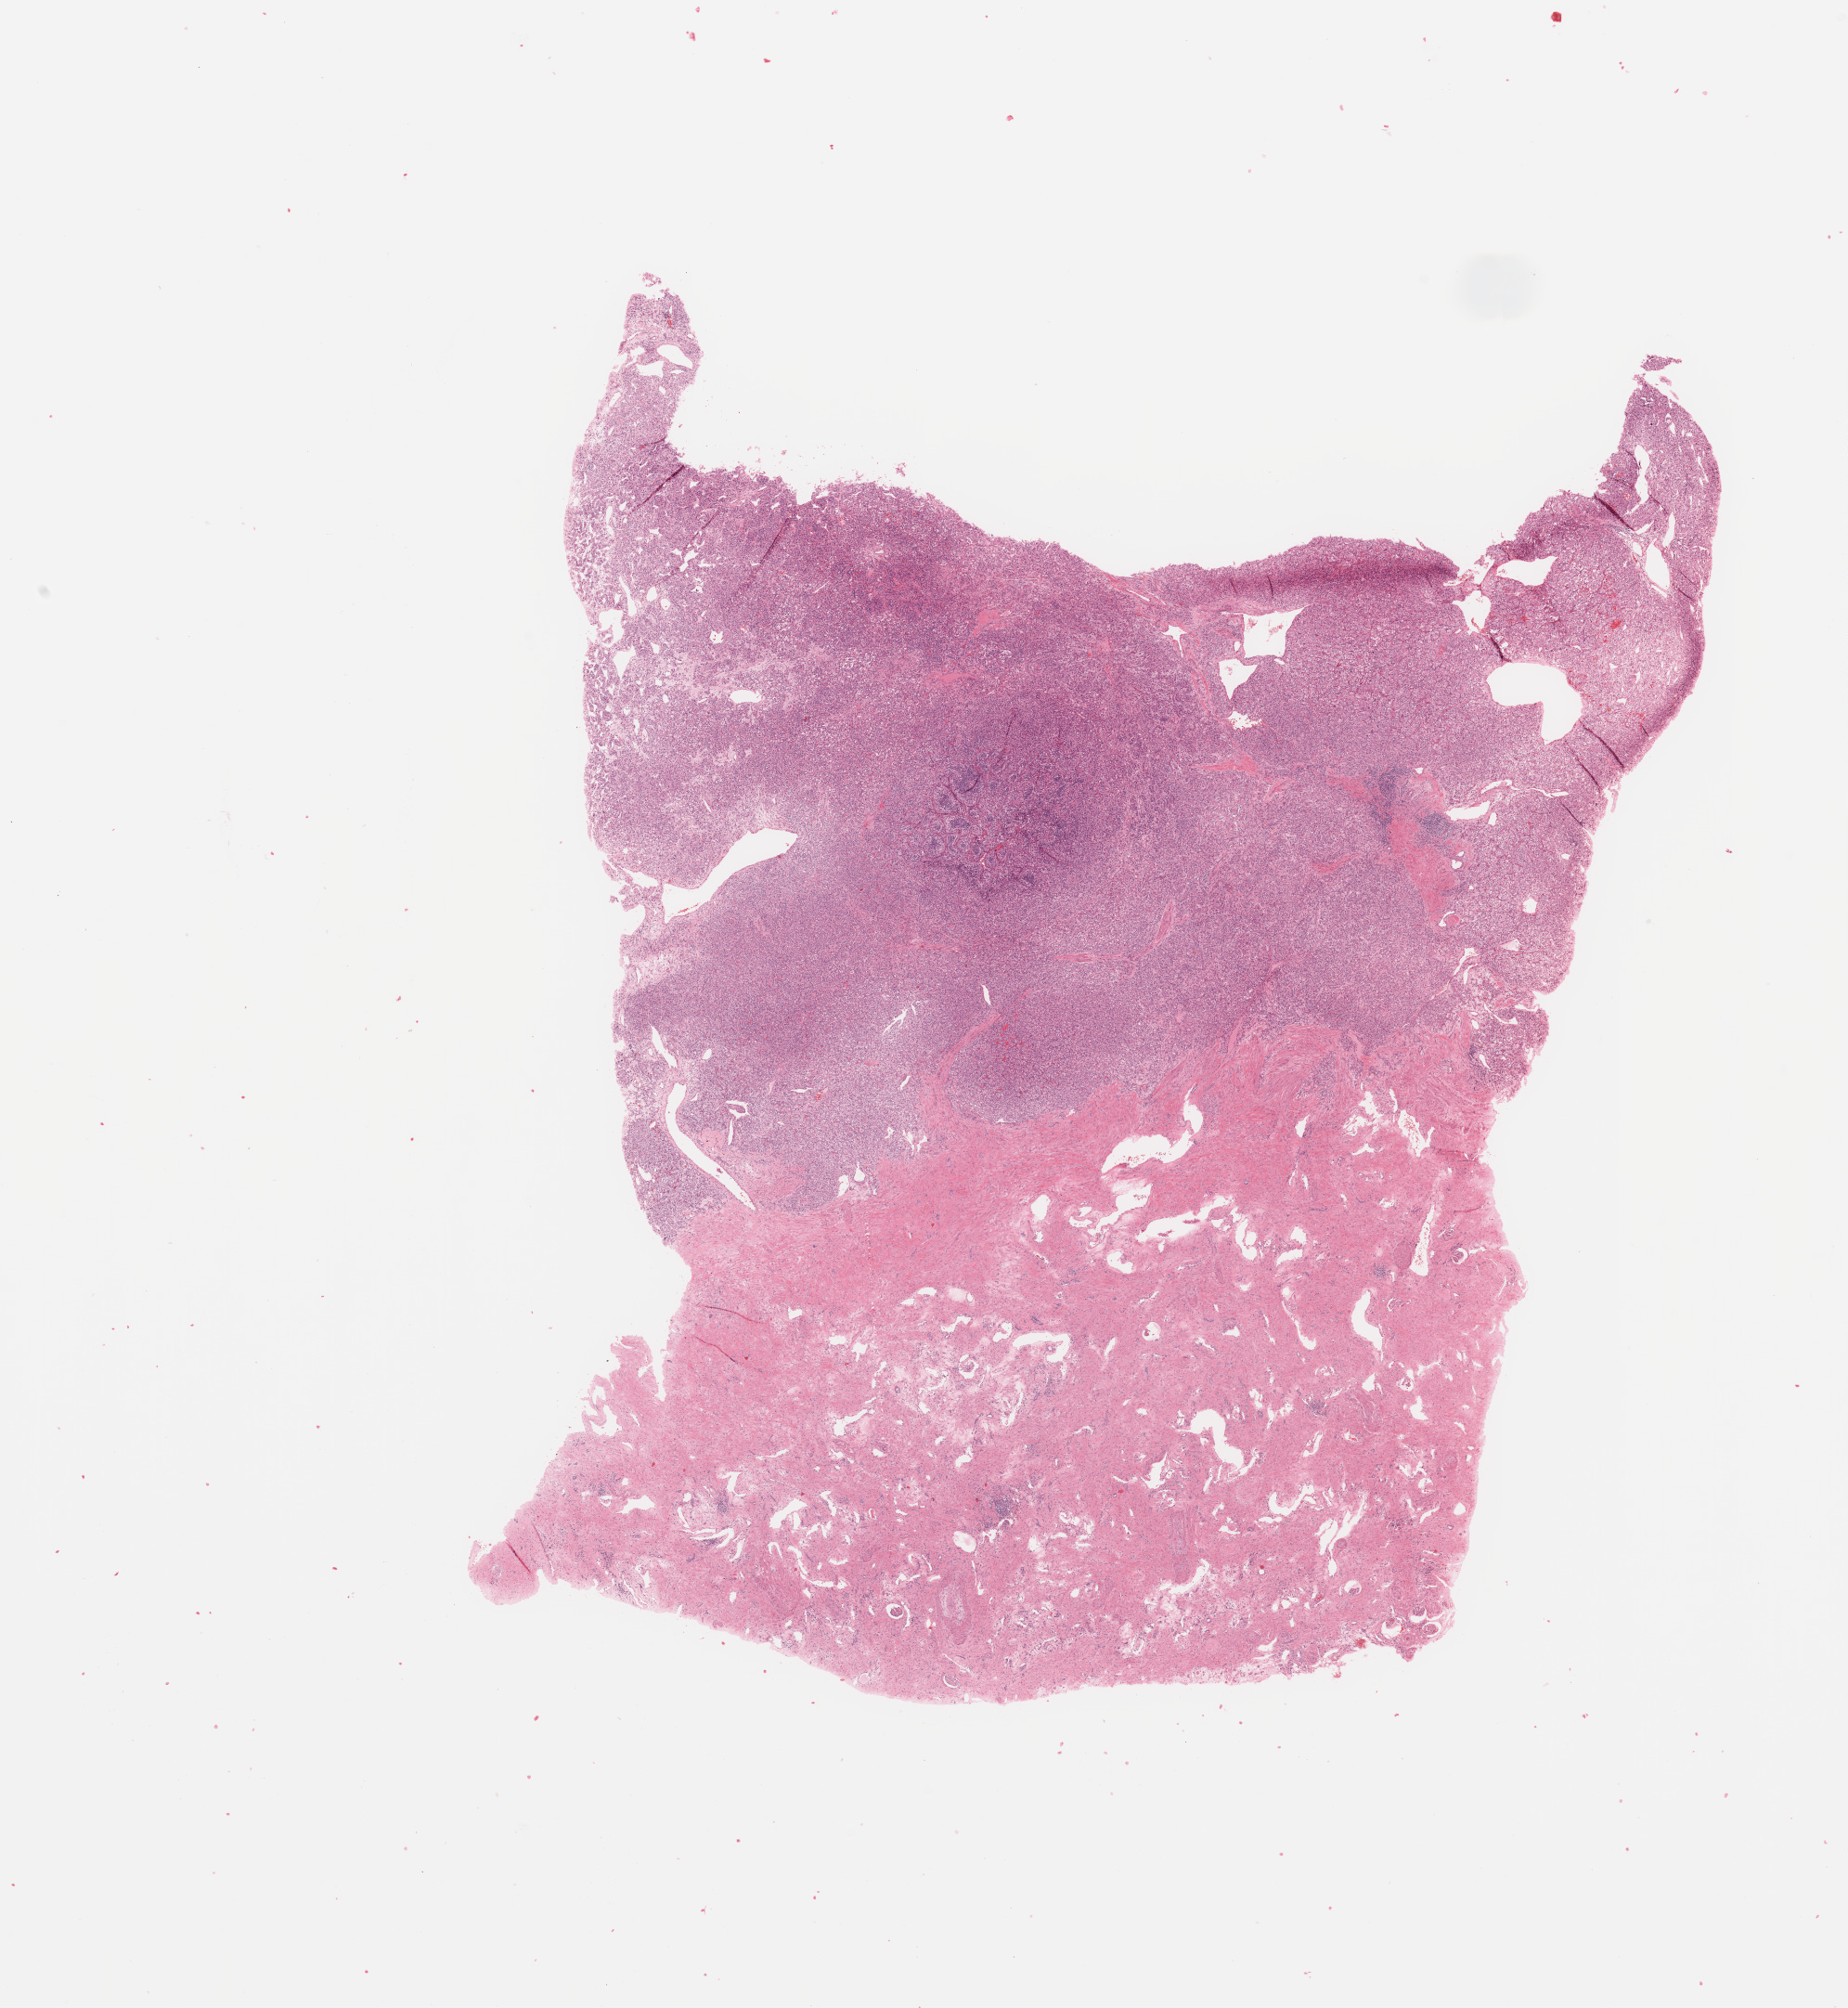
H&E-stained whole-slide image — low-resolution overview of the scanned area, about 15.8 x 17.1 mm; tumour tissue sample, sampled site: kidney. 52-year-old male patient. Composition of this section per pathologist review: tumour nuclei 80%, necrosis 5%.
Diagnosis: Renal cell carcinoma, NOS.